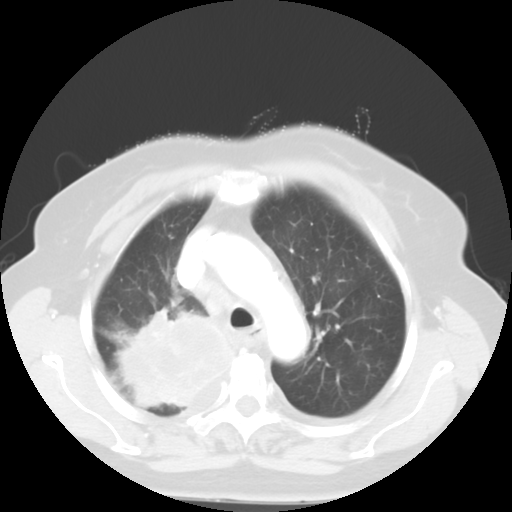
Chest CT, one axial slice; position 40 of 52 along the scan axis; 120 kVp; lung window (W 1500 / L -600 HU); 5 mm slice thickness; 512 × 512 image matrix. Female patient, age 81 years. From the clinical record (not read from this slice): clinical TNM (as recorded): T4 N3 M1b.
Annotated regions visible in this slice (rectangle marked by the reading radiologist):
- lung tumour (recorded histology: adenocarcinoma): bounding box [x1, y1, x2, y2] px = [117, 301, 237, 412]